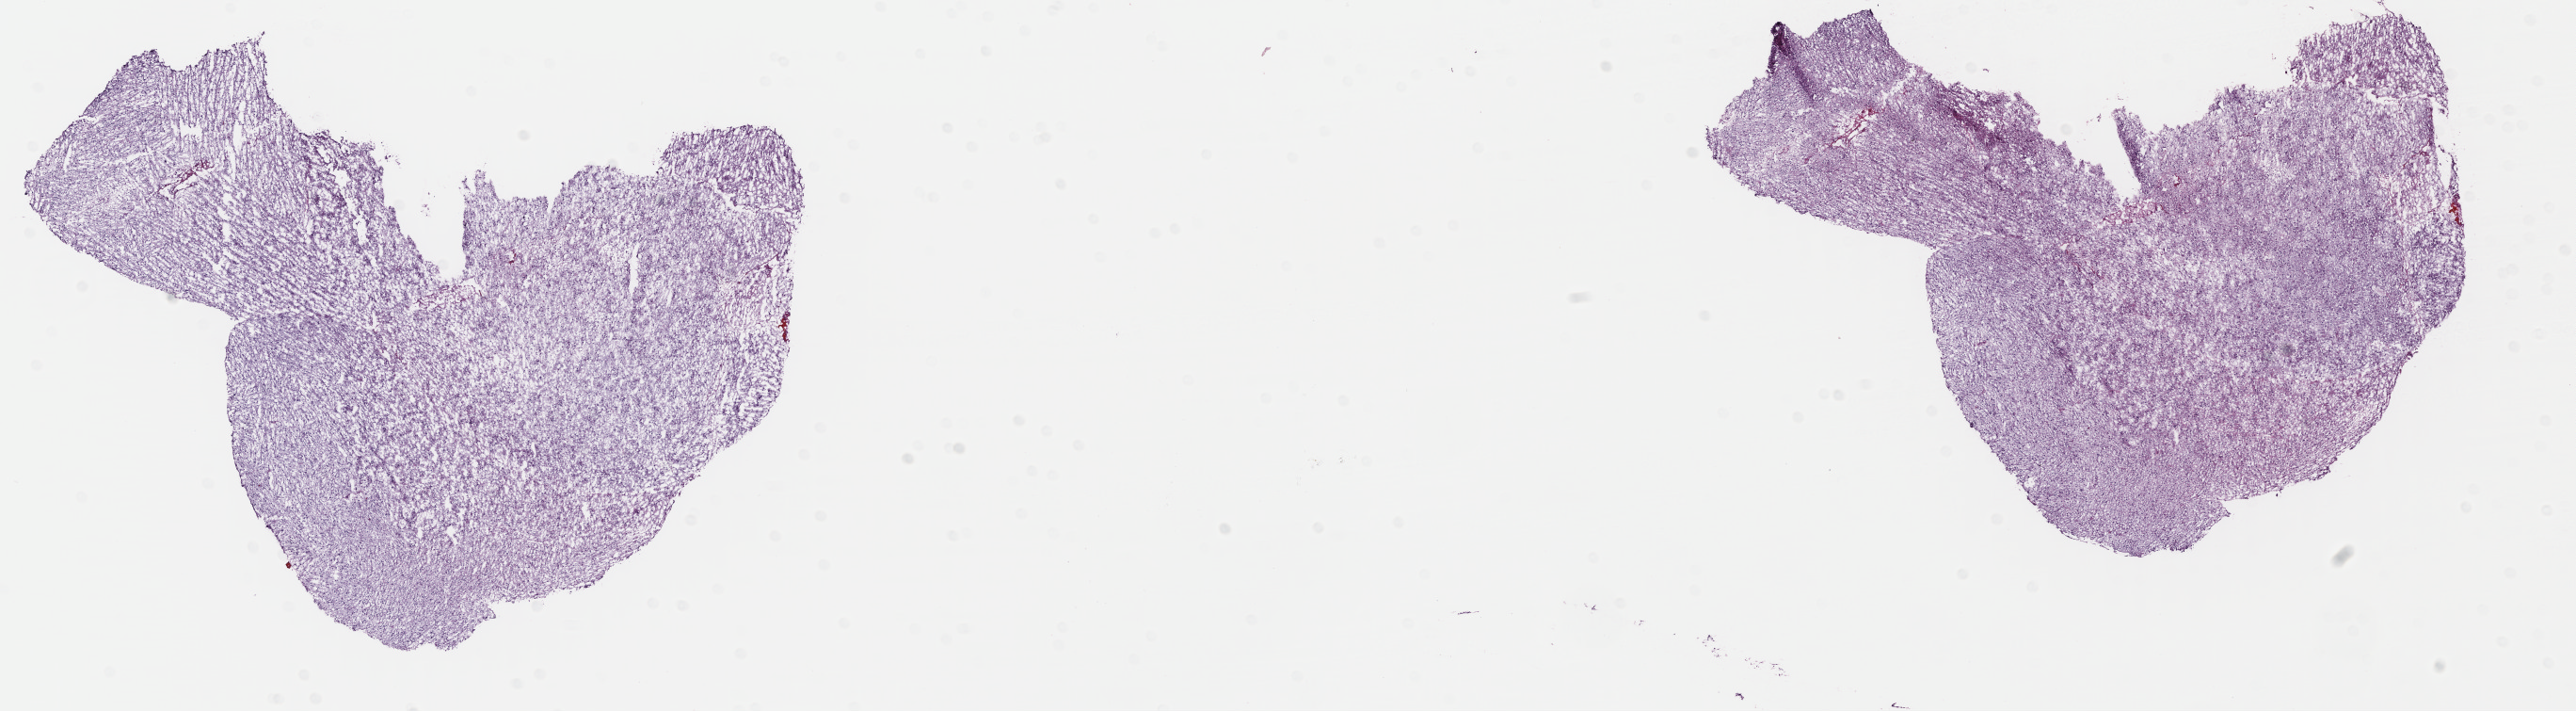
Whole-slide histology image, Hematoxylin and eosin (H&E) stained, whole scanned area (about 21.5 x 5.9 mm) shown as a low-resolution overview. Frozen section from the top of the tissue portion. Primary tumour sample from the brain. Patient: male, age at initial diagnosis 30 years. Histologic grade: G2 (moderately differentiated). Composition of this section per pathologist review: tumour cells 60%, tumour nuclei 85%, normal cells 0%, stromal cells 40%, necrosis 0%. Infiltration values recorded for this section: lymphocyte infiltration 0%, monocyte infiltration 0%, neutrophil infiltration 0%.
Laterality: left. Pathologic diagnosis: Astrocytoma, NOS (cerebrum).